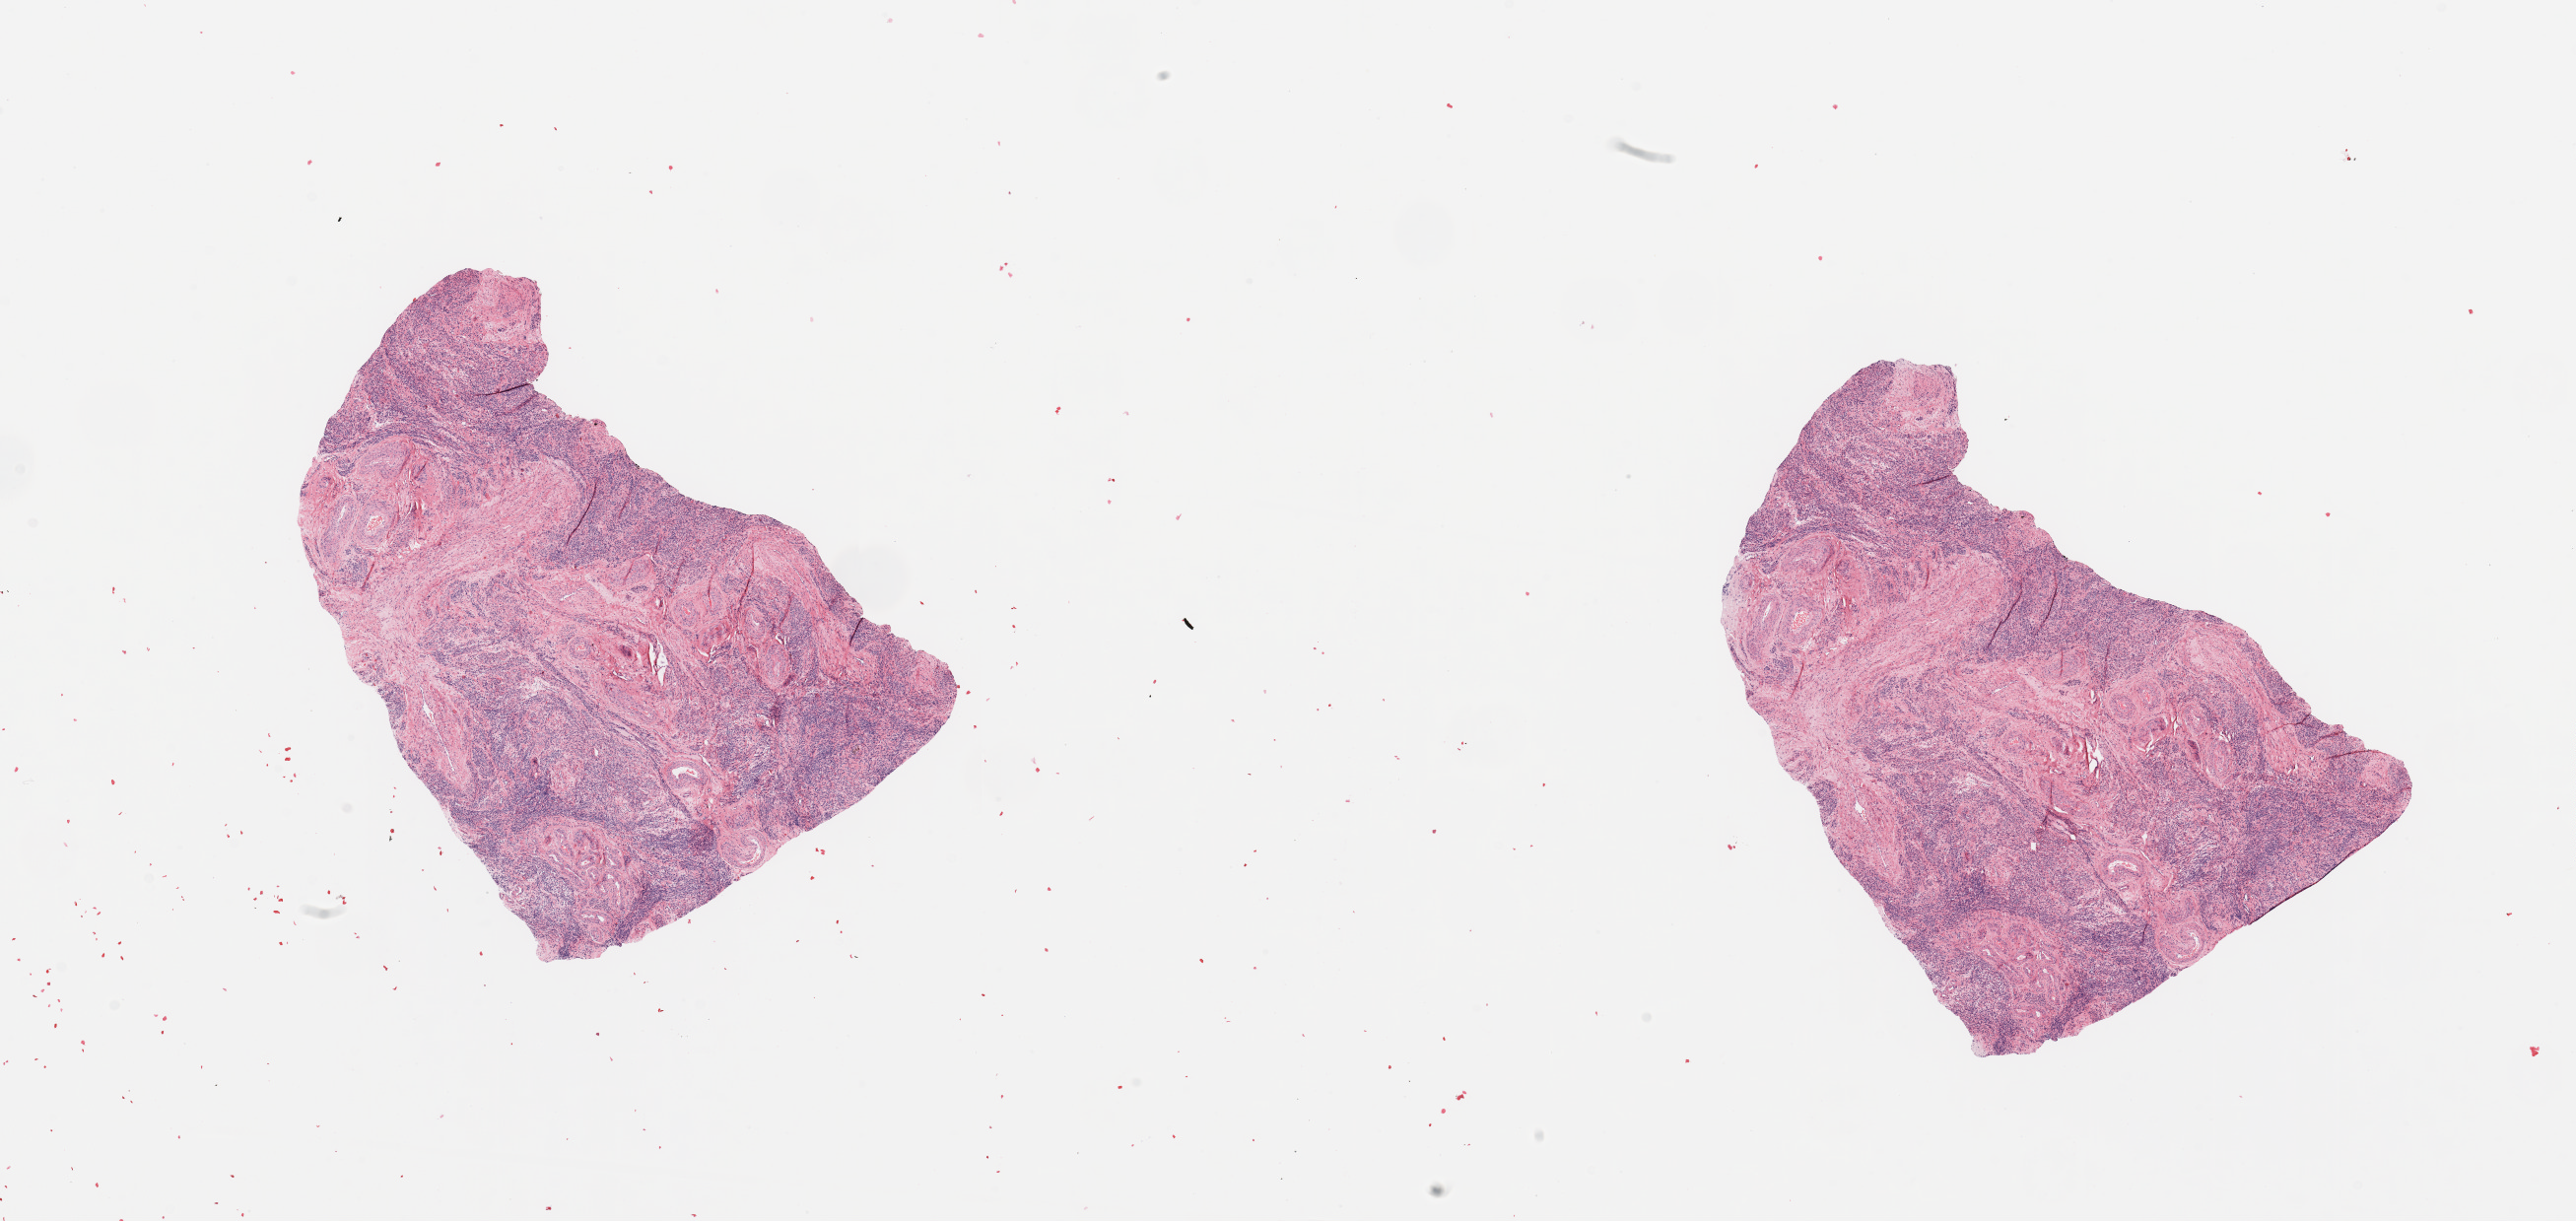
Whole-slide histology image, Hematoxylin and eosin (H&E) stained — whole scanned area (about 20.7 x 9.8 mm, from a 20x scan) shown as a low-resolution overview; uterus, normal (non-tumour) tissue. Female, 77 y/o.
This section: normal (non-tumour) tissue from the same patient. Patient diagnosis: Endometrioid adenocarcinoma, NOS.